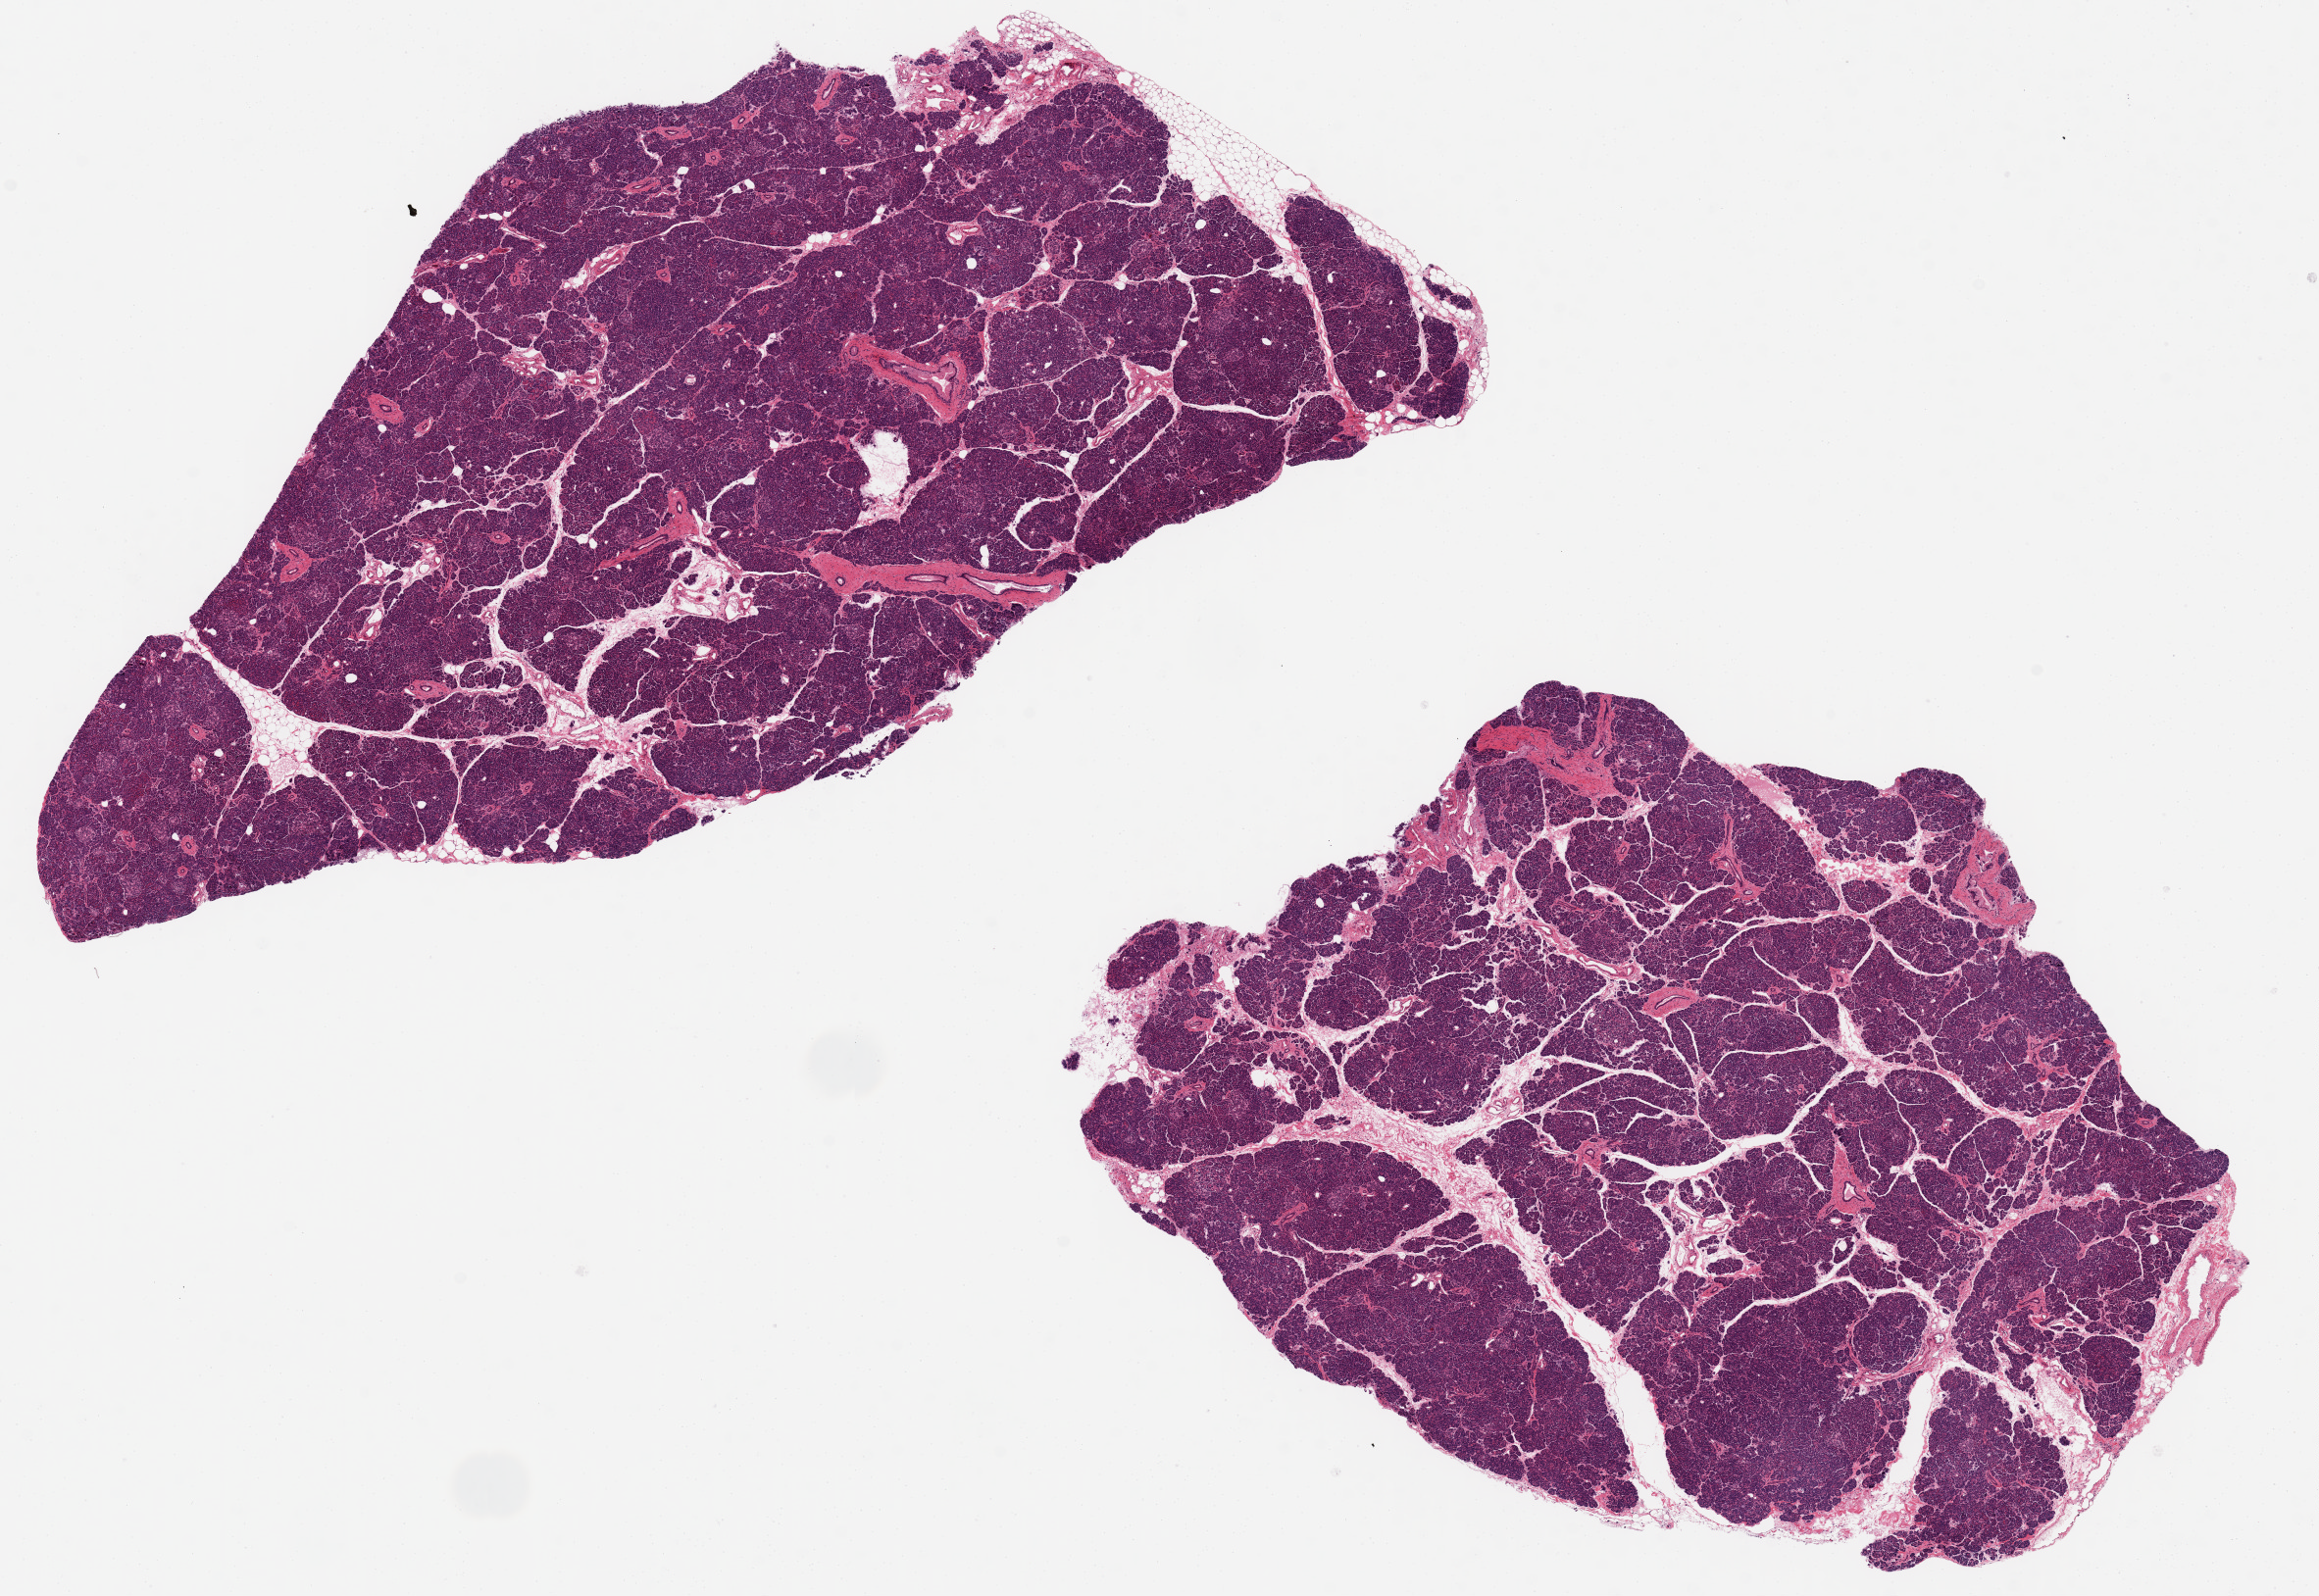
Hematoxylin and eosin (H&E) whole-slide image, brightfield — shown as a low-resolution overview of the whole scanned area (about 18.7 x 12.9 mm, acquisition: 20x scan), PAXgene-fixed paraffin-embedded (PFPE) section, section of pancreas (target tissue), tissue donor sample. Female donor.
- reviewer comment on this tissue sample: 2 aliquots, ~10x7mm. Remarkably well-preserved, minimal fat (<5%)